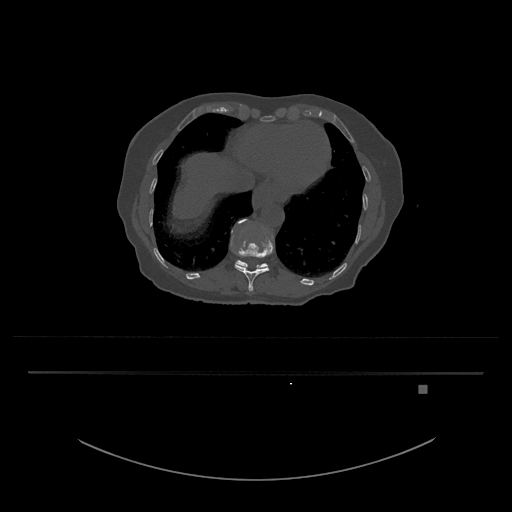
CT including the spine, one axial slice. Slice 649 of 797 in the series (ordered by position). Bone window (W 1800 / L 400 HU). 0.5 mm slice thickness. 512 × 512 image matrix, field of view 500 × 500 mm. Patient: female, 57 years. Case-level facts recorded for this patient, not image findings: primary cancer: cervical.
Annotated regions visible in this slice (semi-automatic segmentation, software-assisted and operator-edited):
- T11 vertebra: bounding box (x1, y1, x2, y2) in pixels: (231, 219, 273, 292)
- T12 vertebra: (235, 260, 268, 271)